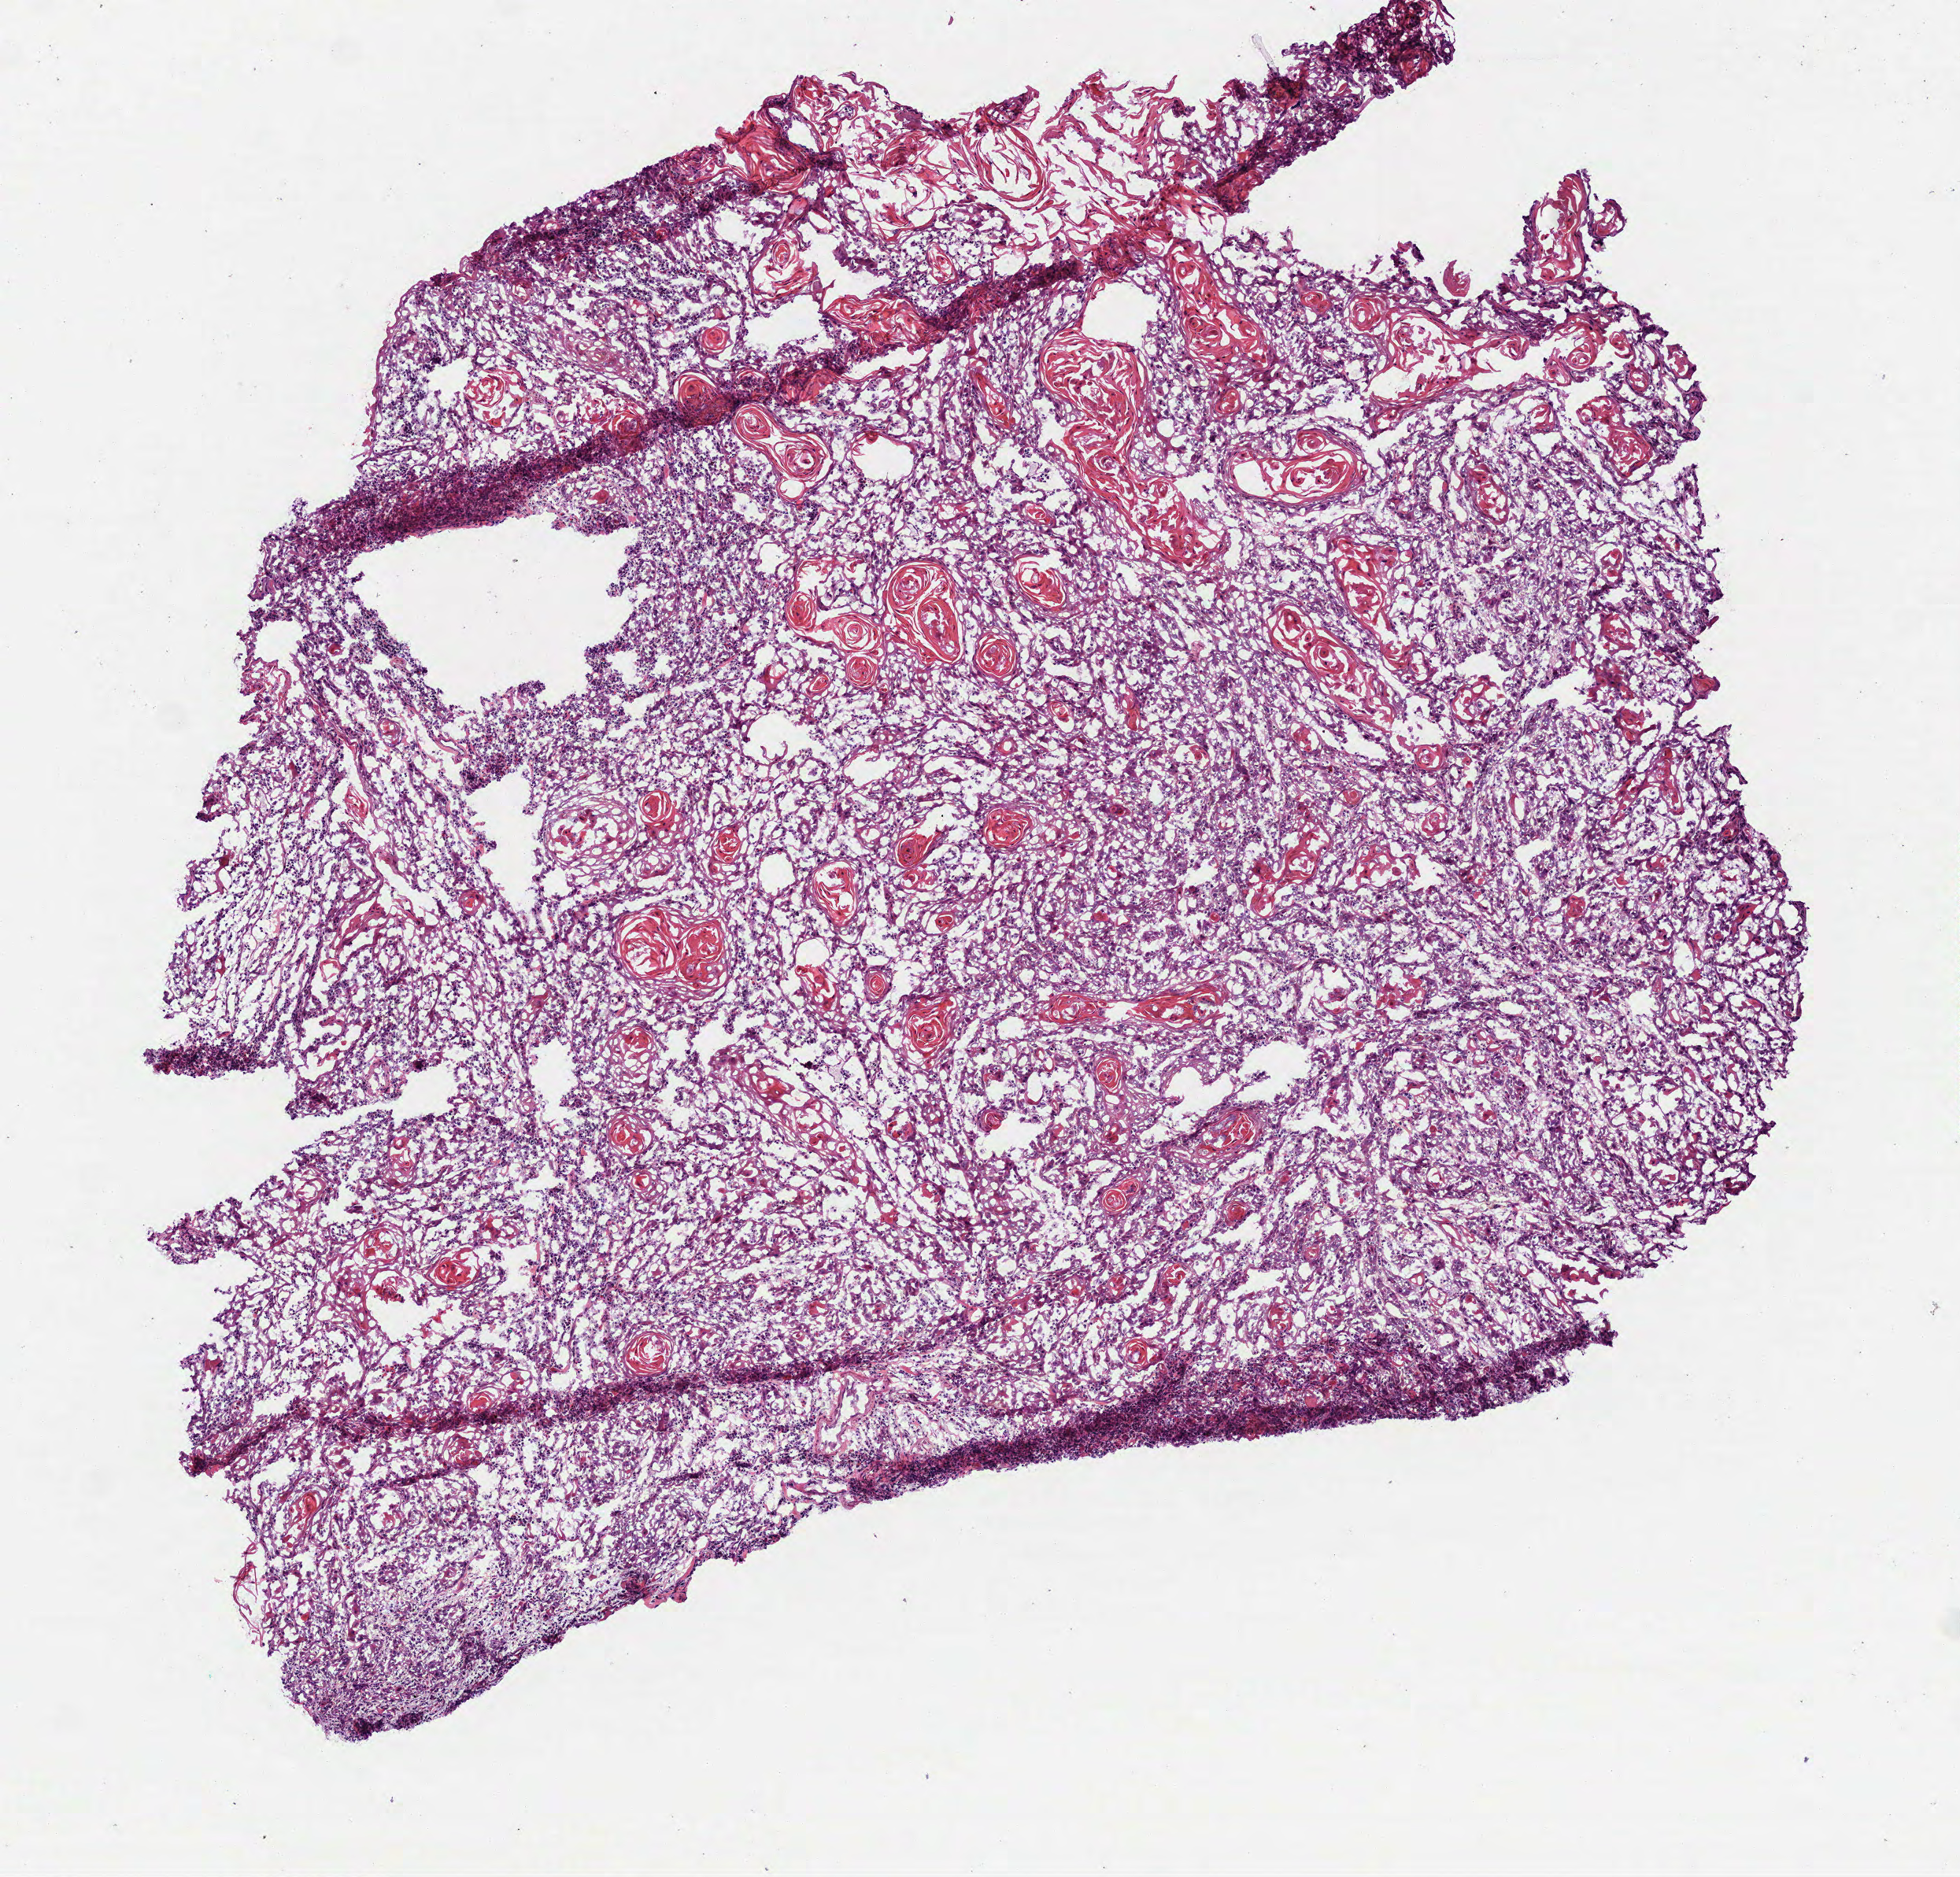
Digitized H&E-stained tissue section (whole slide), low-resolution overview of the scanned area, about 5.0 x 4.8 mm (acquisition: 40x scan); frozen section from the top of the tissue portion; head and neck, primary tumour sample. Female patient; age at initial diagnosis 58 years. Histologic grade: G2 (moderately differentiated). Pathologist review of this section (percent, as recorded): tumour cells 90%, tumour nuclei 65%, normal cells 0%, stromal cells 10%, necrosis 0%.
Diagnosis: Squamous cell carcinoma, NOS (tongue, NOS). AJCC pathologic stage: IVA (7th edition).